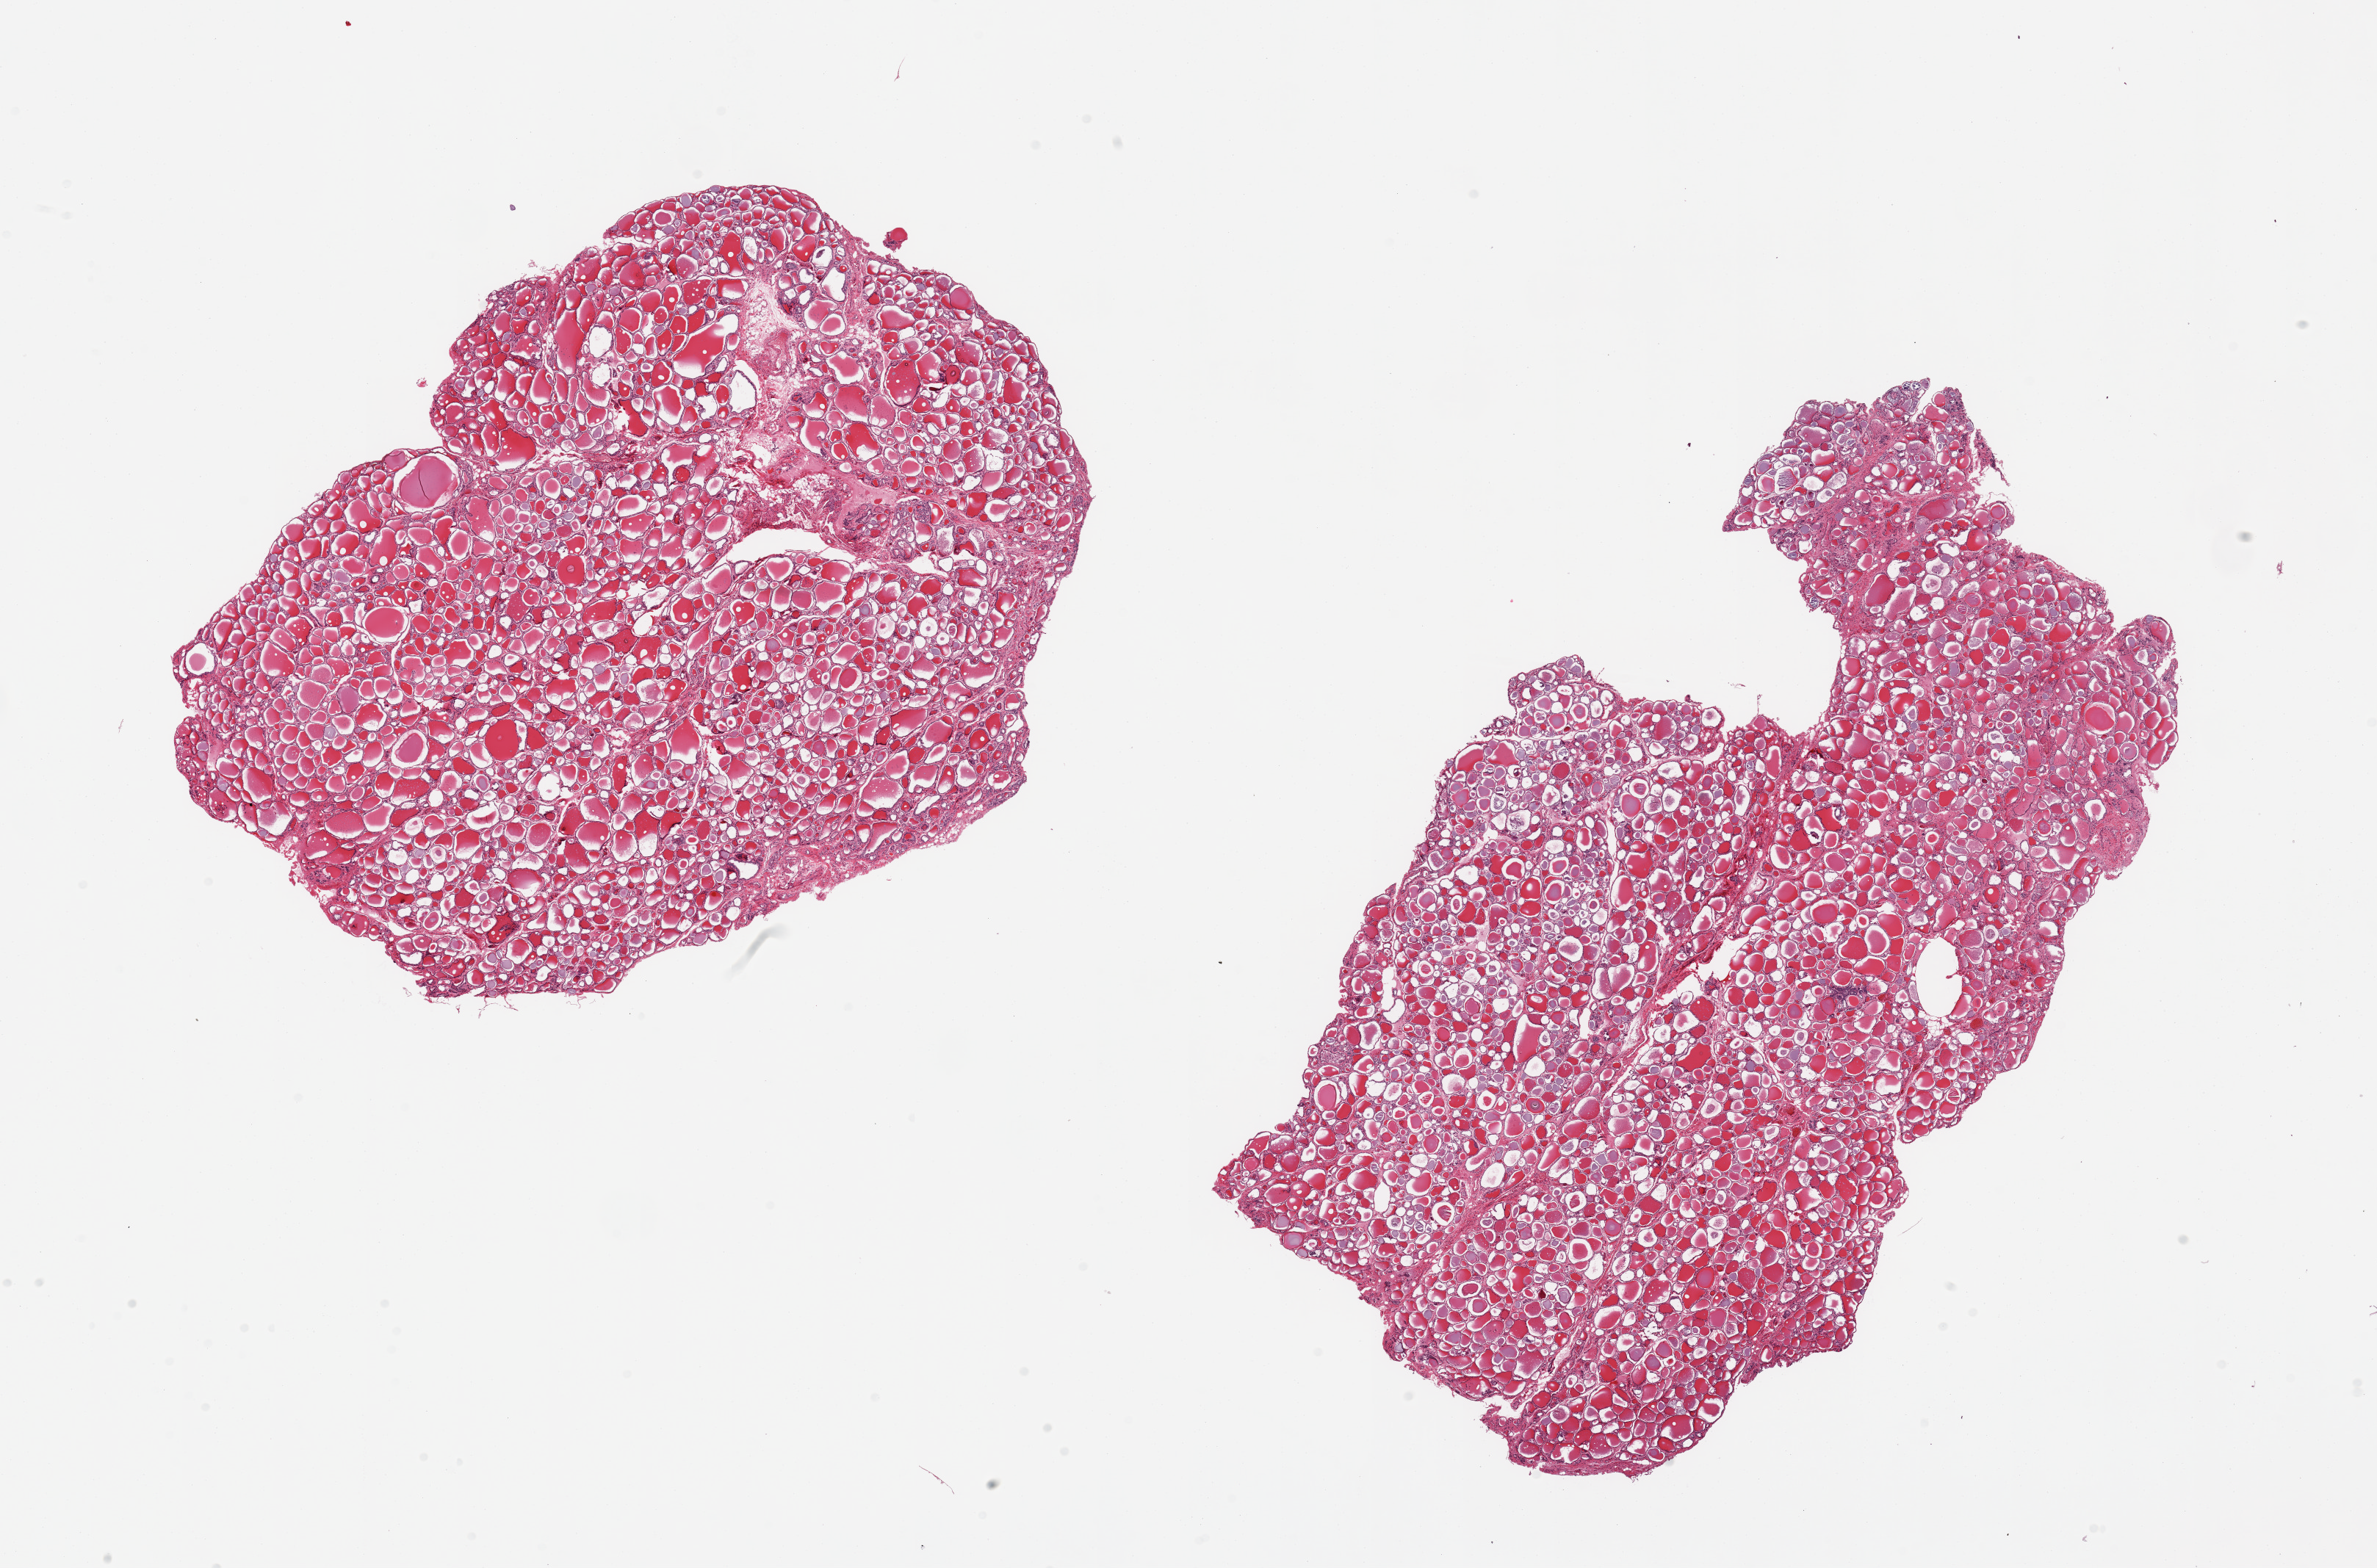
Whole-slide image, H&E stain — whole scanned area (about 25.6 x 16.9 mm, from a 20x scan) shown as a low-resolution overview, PAXgene-fixed, paraffin-embedded tissue, sampled site (target tissue): thyroid, tissue donor sample. Donor sex: male.
* pathologist's review note for this sample: 2 pieces, no significant abnormalities